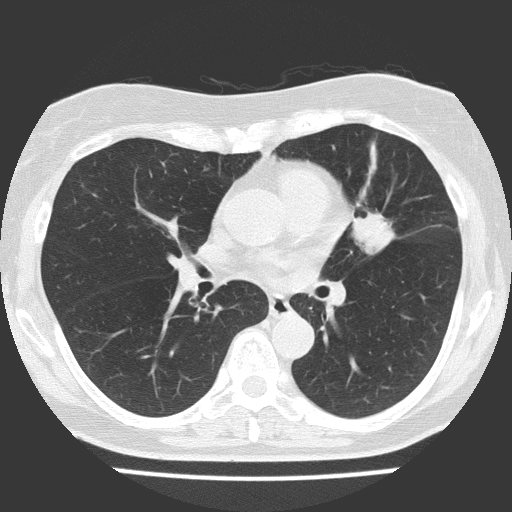
Low-dose screening chest CT, one axial slice; position 79 of 151 along the scan axis; reconstruction kernel FC51; 120 kVp; lung window (W 1500 / L -600 HU); 512 × 512 image matrix.
Structures marked on this image (expert manual segmentation):
- lesion 1 (tumor, upper lobe of left lung): box from (x=353, y=212) to (x=395, y=255) px